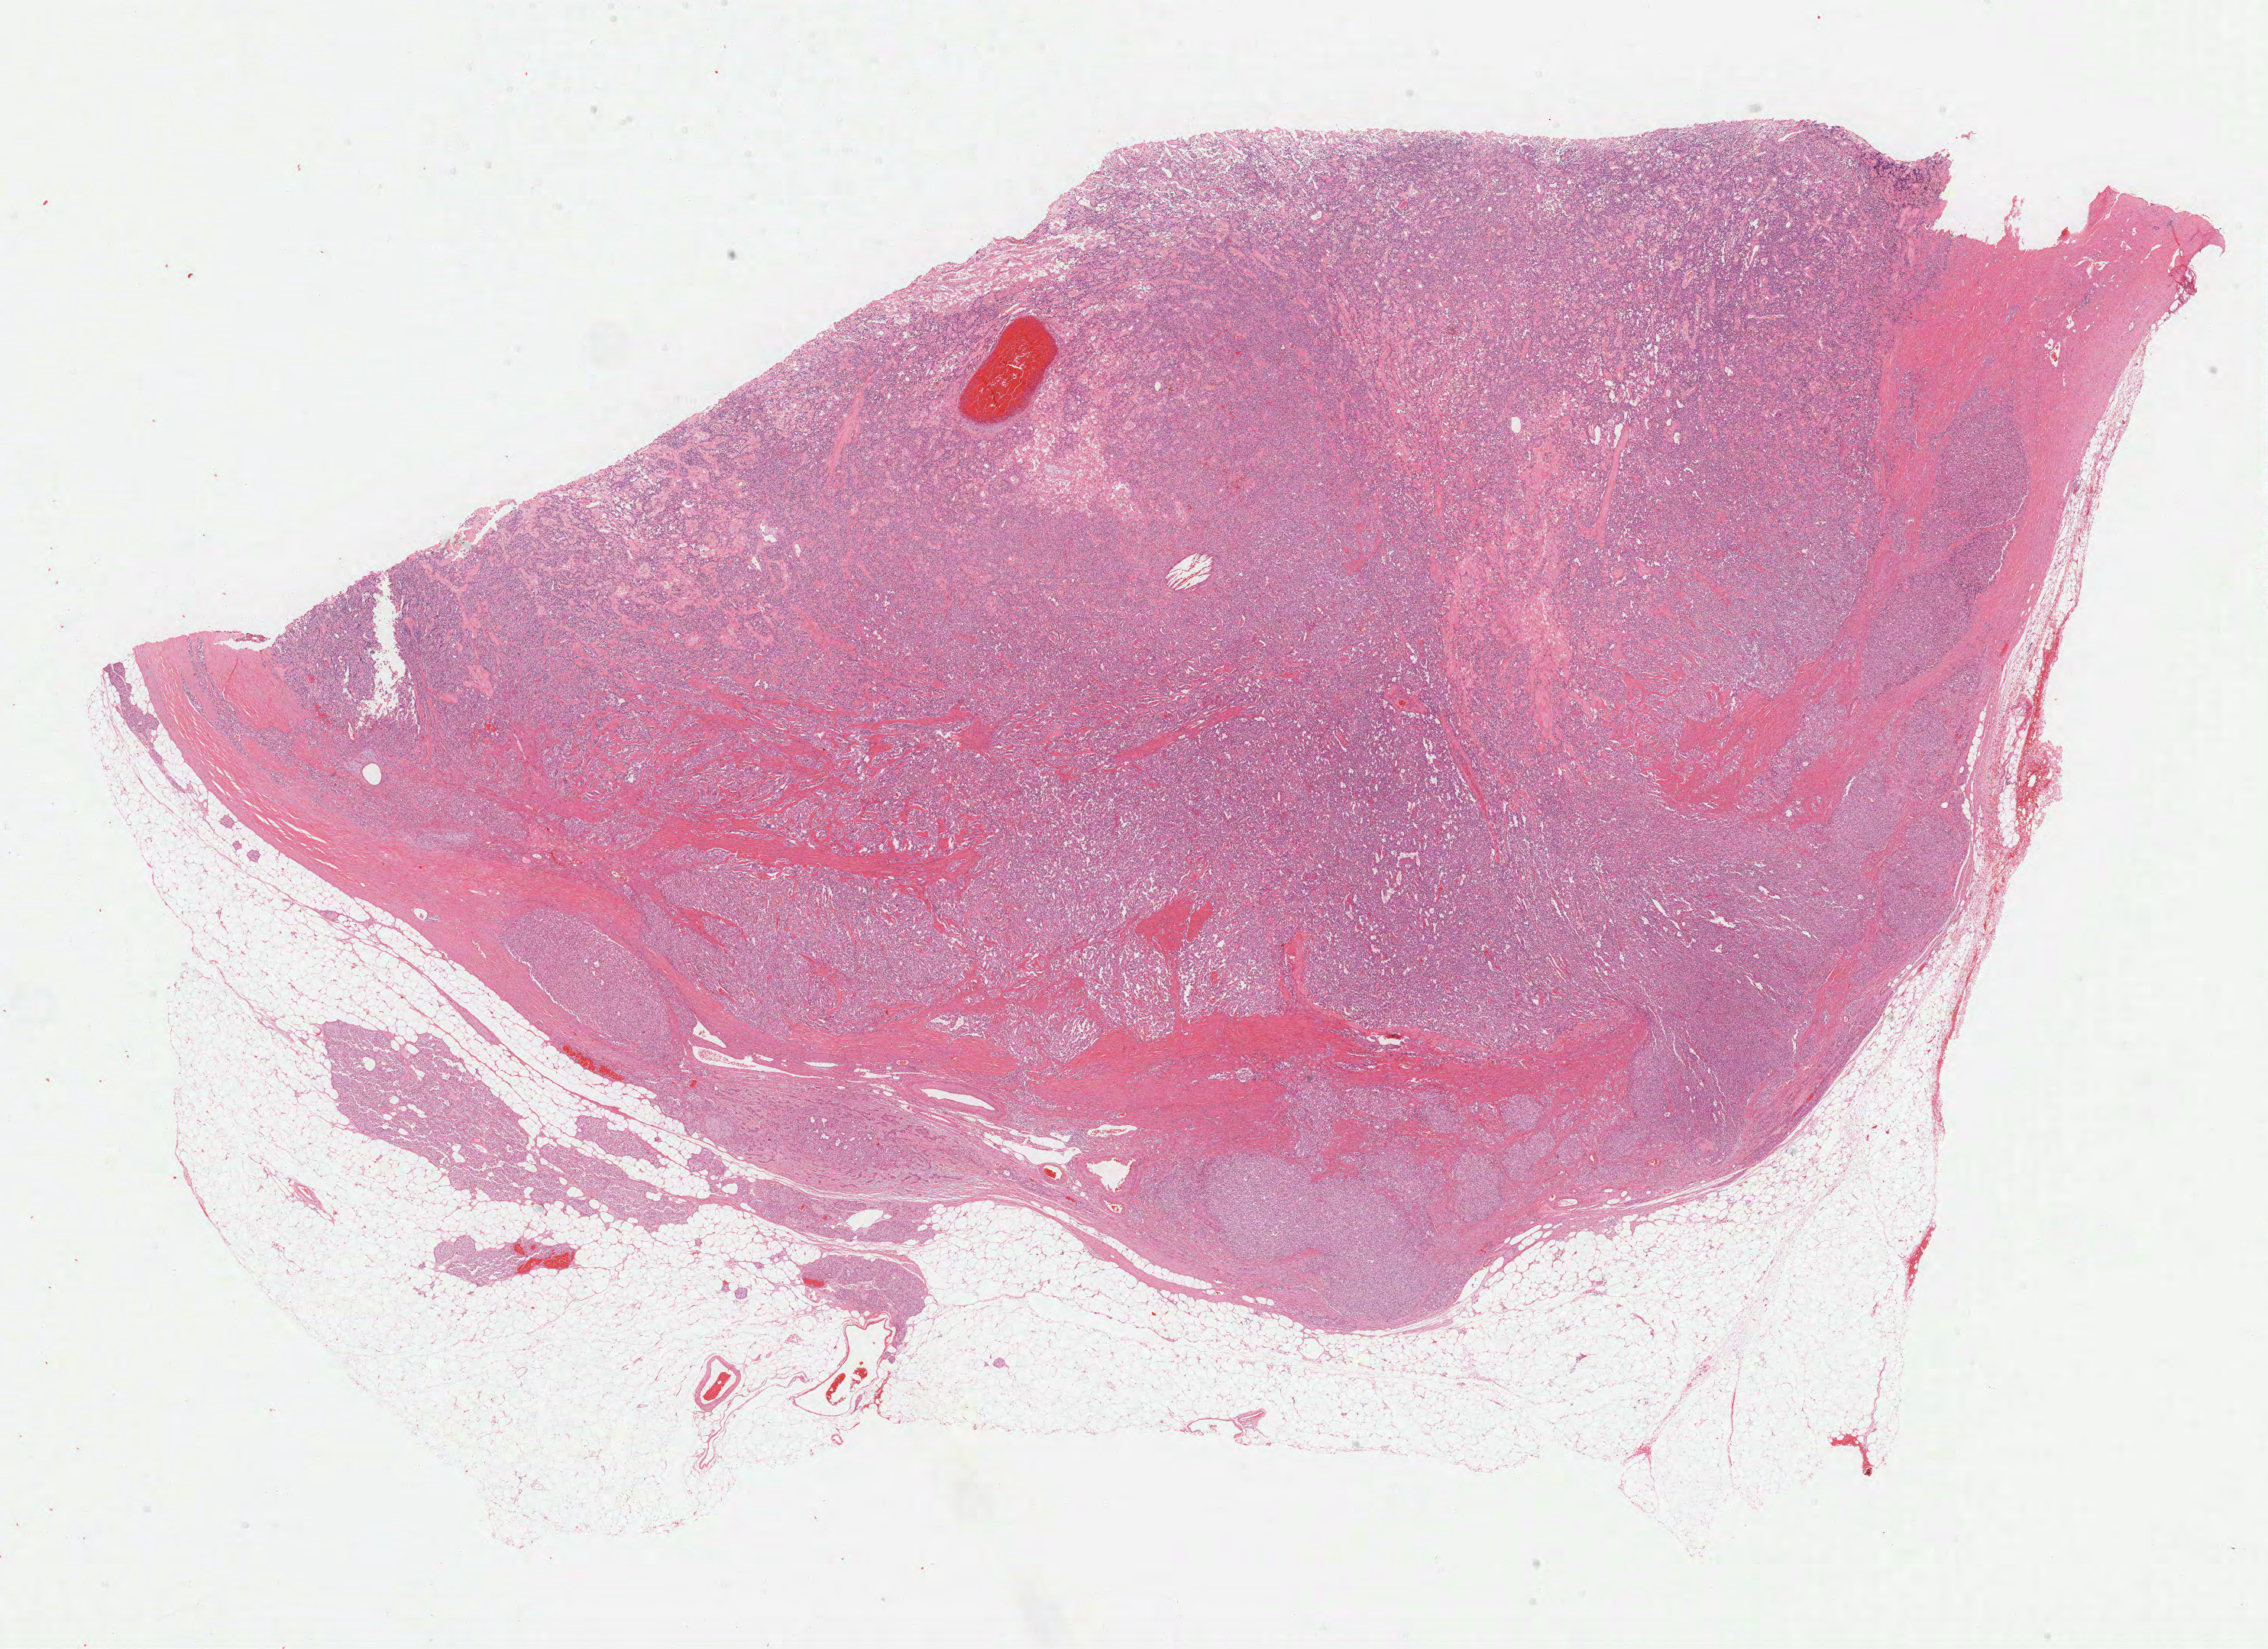
H&E-stained whole-slide image, low-resolution overview of the scanned area, about 24.0 x 17.4 mm (from a 40x scan), FFPE section, pancreas, primary tumour sample. Patient: female, age at initial diagnosis 62 years. Histologic grade: G2 (moderately differentiated).
AJCC pathologic stage: IB (6th edition). Diagnosis: Neuroendocrine carcinoma, NOS (body of pancreas).